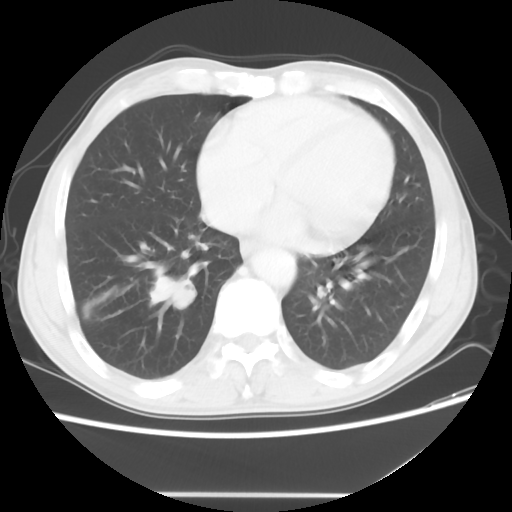
Chest CT, one axial slice; position 18 of 56 along the scan axis; reconstruction kernel STANDARD; 120 kVp; lung window (W 1500 / L -600 HU); 512 × 512 image matrix, field of view 344 × 344 mm. Male patient, age 65 years. Case-level facts recorded for this patient, not image findings: clinical TNM (as recorded): T1c N3 M0.
Structures marked on this image (bounding box drawn by a radiologist):
- lung tumour (recorded histology: small cell carcinoma): box from (x=148, y=264) to (x=204, y=312) px